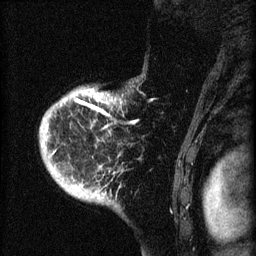
Breast MRI (dynamic contrast-enhanced), one sagittal slice; position 55 of 60 along the scan axis; dynamic contrast-enhanced series, image 2 of 4 at this slice position (ordered by acquisition); 1.5 T; TE 4.2 ms, TR 8.2 ms; 2 mm slice thickness; 256 × 256 image matrix, field of view 180 × 180 mm. Female patient, age 71 years.
Outlined on this slice (semi-automatic segmentation, software-assisted and operator-edited):
- analysis volume of interest (the breast-tissue region the enhancement analysis was run in; not a lesion): bounding box <39,85,144,190> (left, top, right, bottom; pixels)
- tumour enhancement mask (voxels above the 70 % enhancement threshold inside the analysis volume of interest): <46,93,116,155>